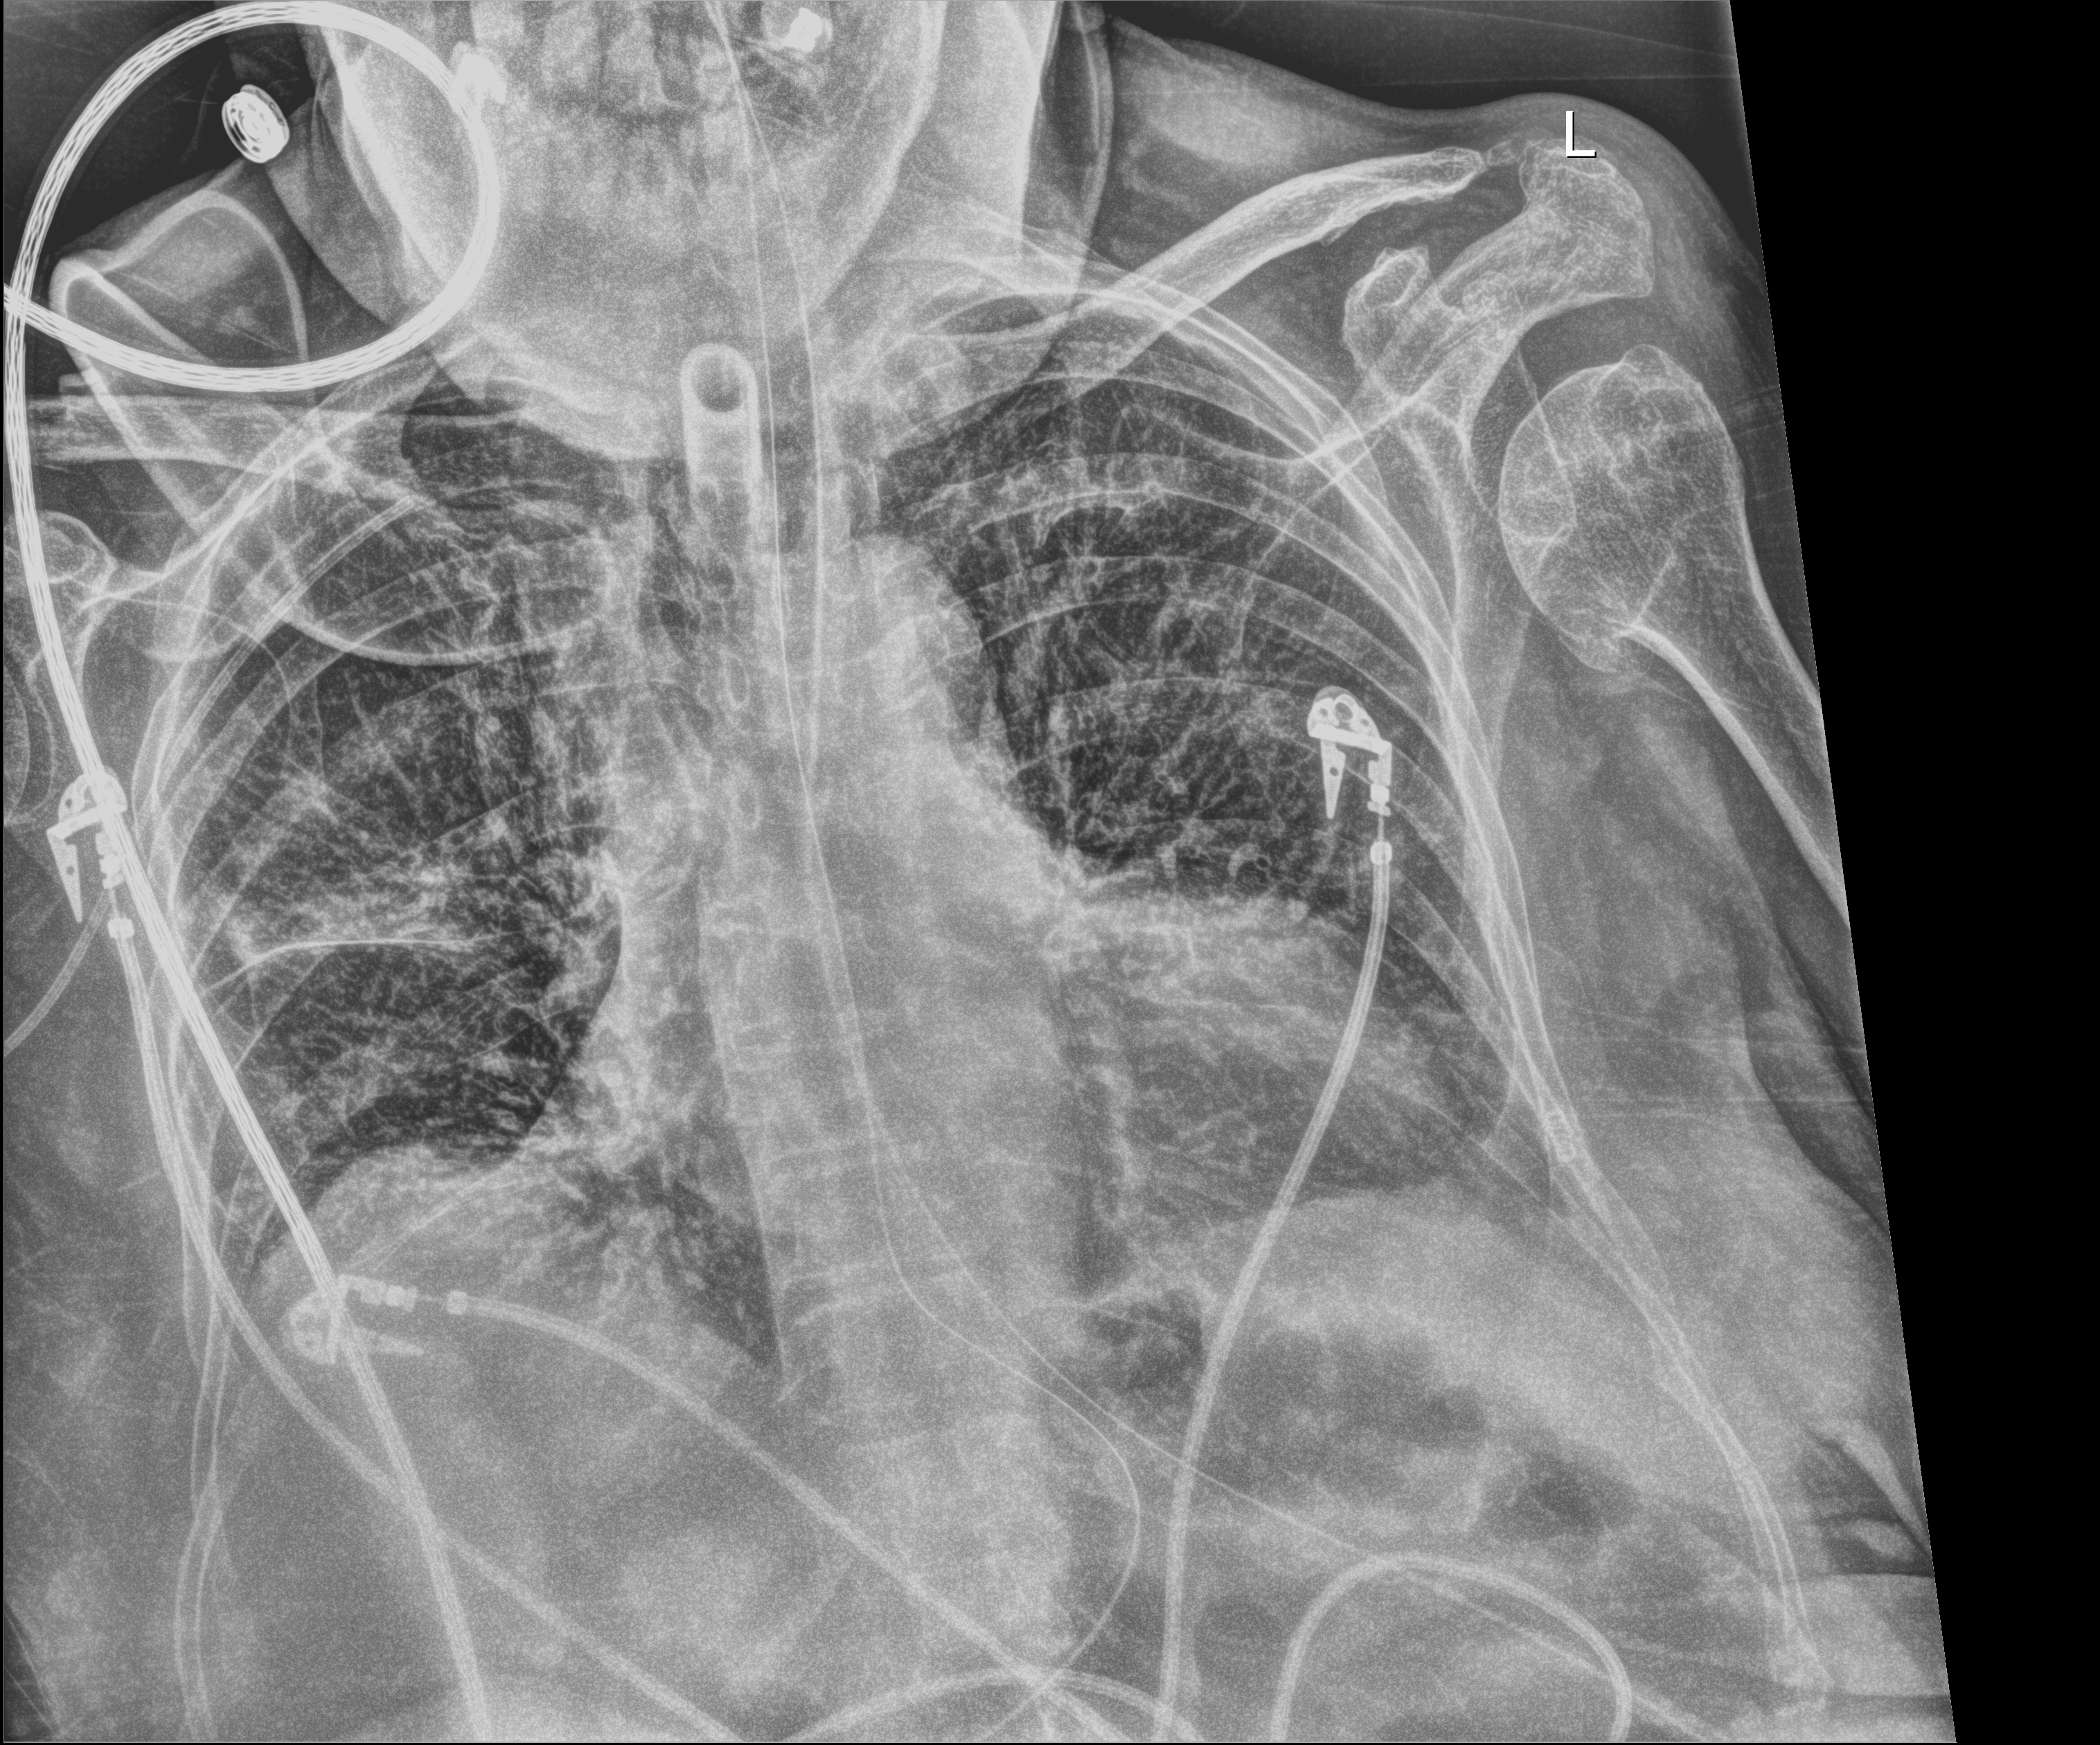
Portable chest radiograph; anteroposterior (AP) projection. Female patient hospitalised with COVID-19, age 75–90 years.
Hospital-stay facts (about this admission, not read from this image; timing relative to this image not recorded): COPD (admission record): no; hypertension (admission record): yes; admitted to intensive care during this hospital stay: yes.